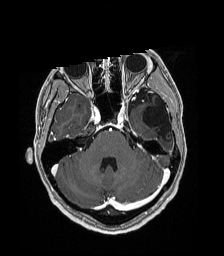
Brain MRI from a brain-tumour surgery series, one axial slice; slice 128 of 192 in the series (ordered by position); T1-weighted post-contrast; 1 mm slice thickness; 224 × 256 image matrix, field of view 224 × 256 mm. Case-level facts recorded for this patient, not image findings: histopathology: Low grade glioma; IDH mutation: no; tumour location: Left Parieto-Occipital Intraventricular.
Outlined on this slice (outlined manually by an expert reader):
- previous resection cavity: bounding box <143,99,170,137> (left, top, right, bottom; pixels)